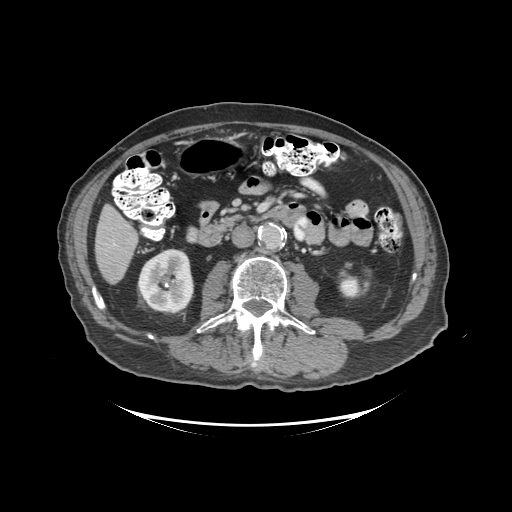
Contrast-enhanced abdominal CT (liver protocol), one axial slice. Position 31 of 99 along the scan axis. Reconstruction kernel STANDARD. 140 kVp. Soft-tissue window (W 400 / L 40 HU). 2.5 mm slice thickness. 512 × 512 image matrix, field of view 460 × 460 mm. Case-level facts recorded for this patient, not image findings: diagnosis: hepatocellular carcinoma (patient treated with transarterial chemoembolisation; whether this scan precedes or follows treatment is not stated here); TNM stage (as recorded): Stage-I; Child-Pugh class: A; tumour differentiation: moderately differentiated; tumour nodularity: uninodular.
Outlined on this slice (semi-automatic segmentation, software-assisted and operator-edited):
- liver parenchyma outside the tumour (the mass and vessels are separate outlines, so this box may not span the whole liver): bounding box [x1, y1, x2, y2] px = [94, 204, 138, 284]